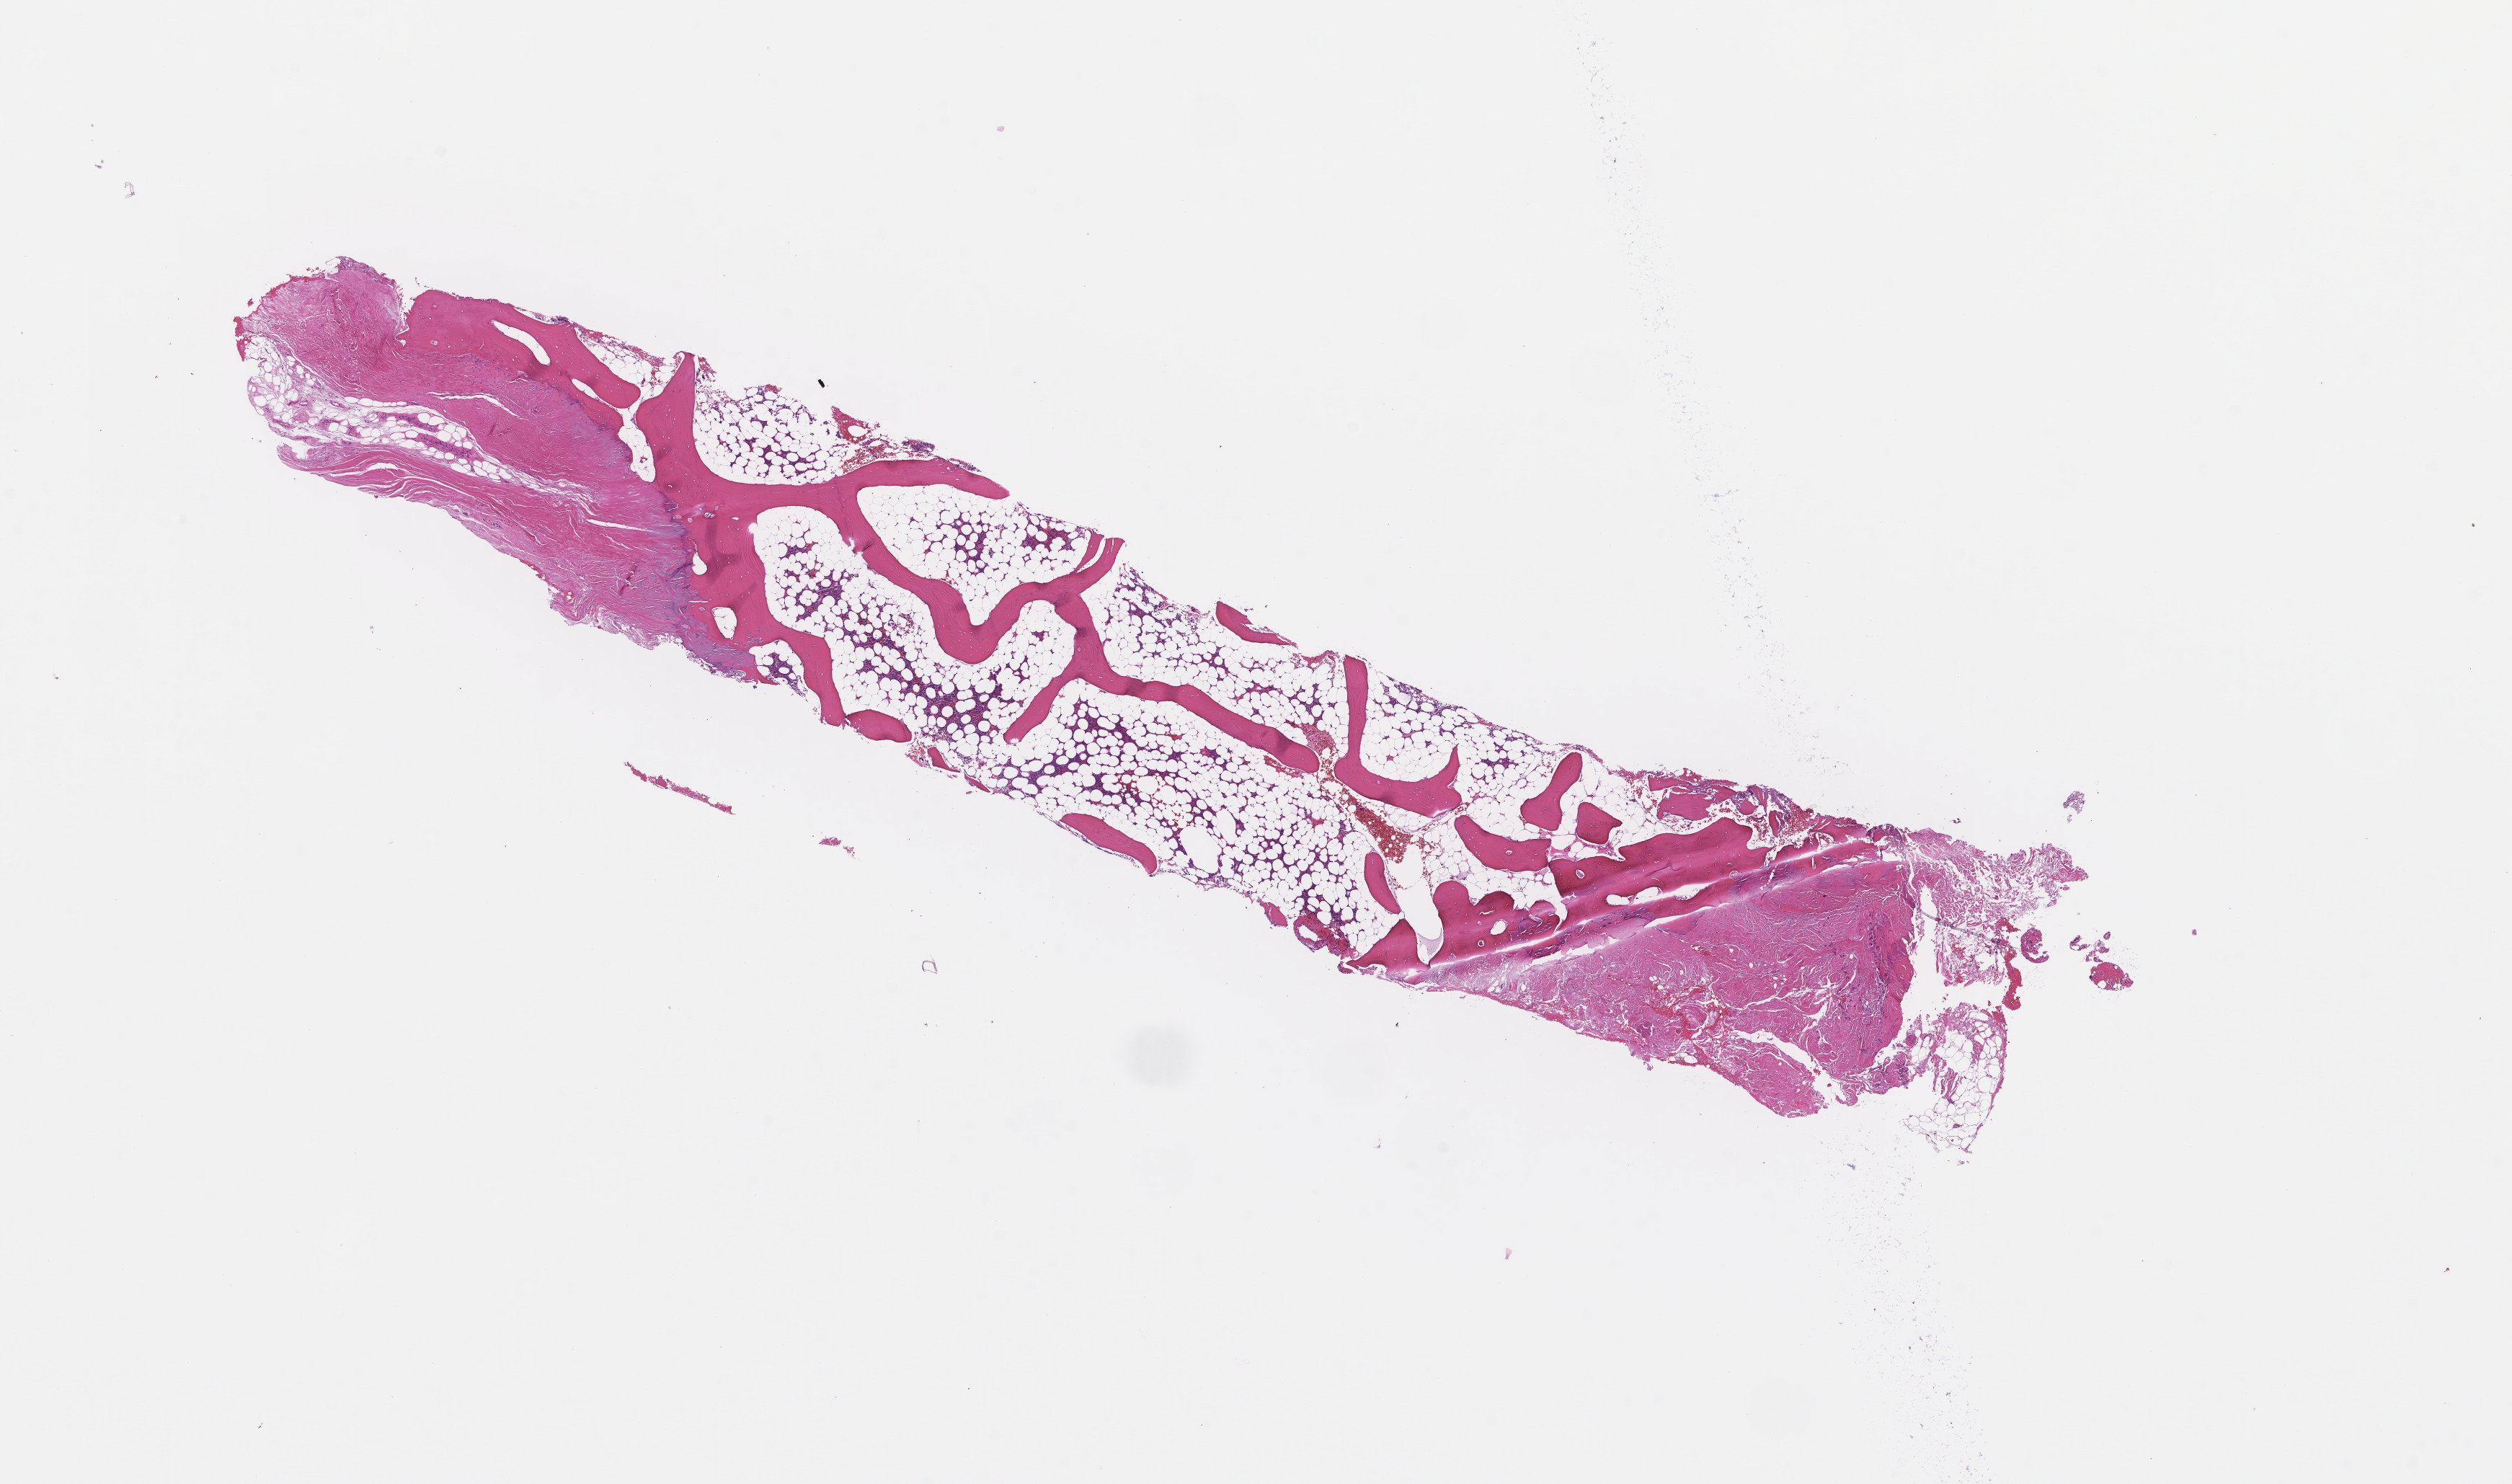
Whole-slide image, H&E stain, whole scanned area (about 14.1 x 8.3 mm) shown as a low-resolution overview. Formalin-fixed paraffin-embedded section. Tissue site: bone marrow. Archival tissue. Patient: male.
* this section: primary tumour tissue
* diagnosis: Plasma Cell Myeloma